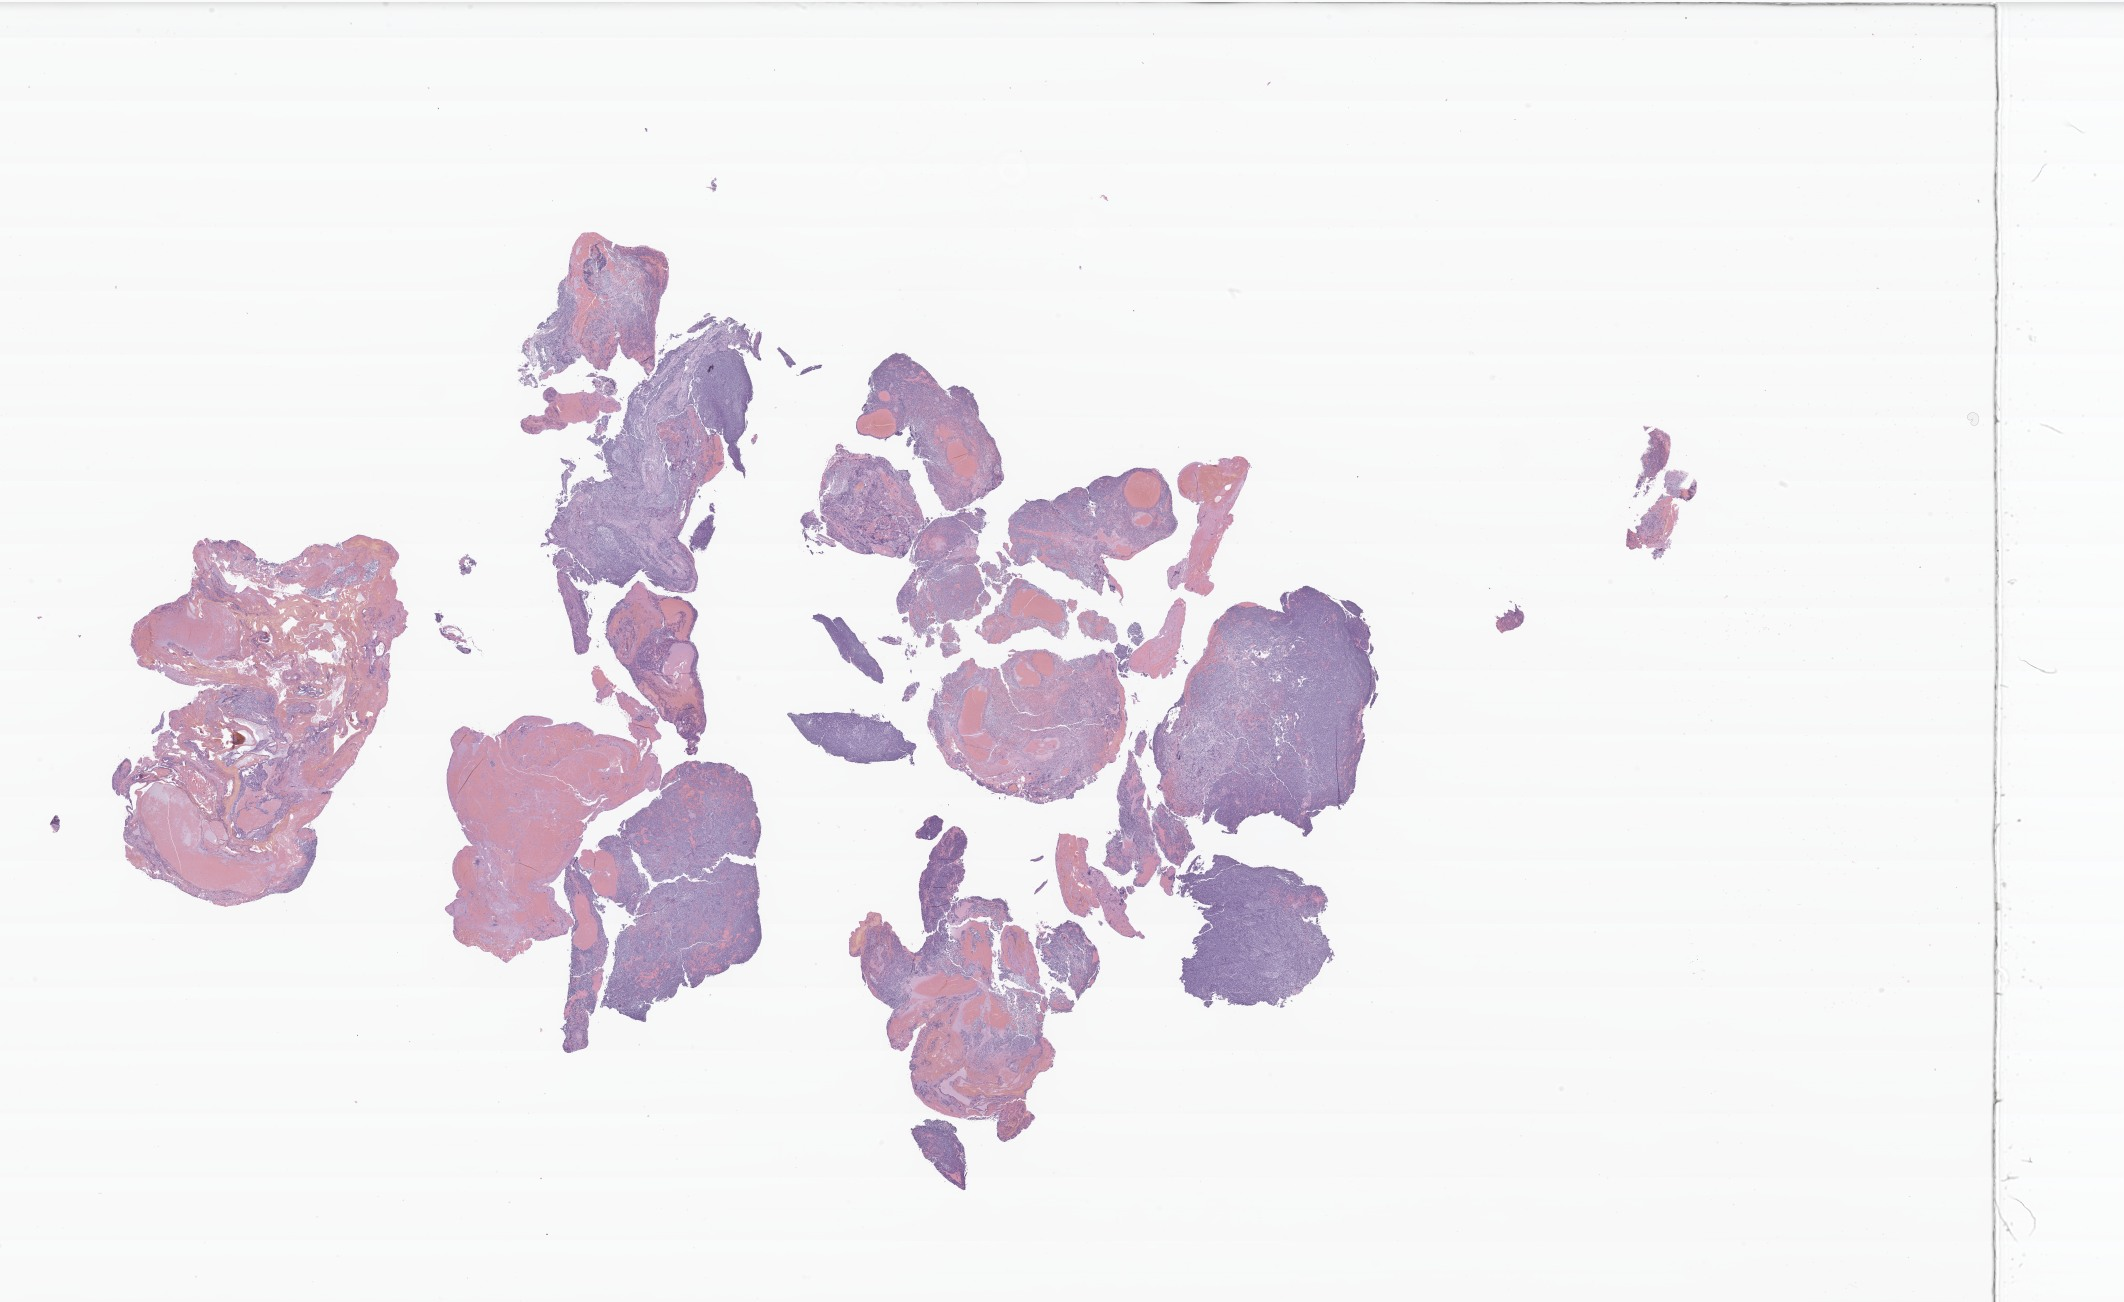
H&E whole-slide image of tumor tissue from the brain, a low-resolution overview of the entire scanned area, about 35.7 x 21.9 mm. Formalin-fixed, paraffin-embedded (FFPE) tissue. Patient male; age 148 months (12 years 4 months).
Recorded diagnosis: Medulloblastoma, NOS.